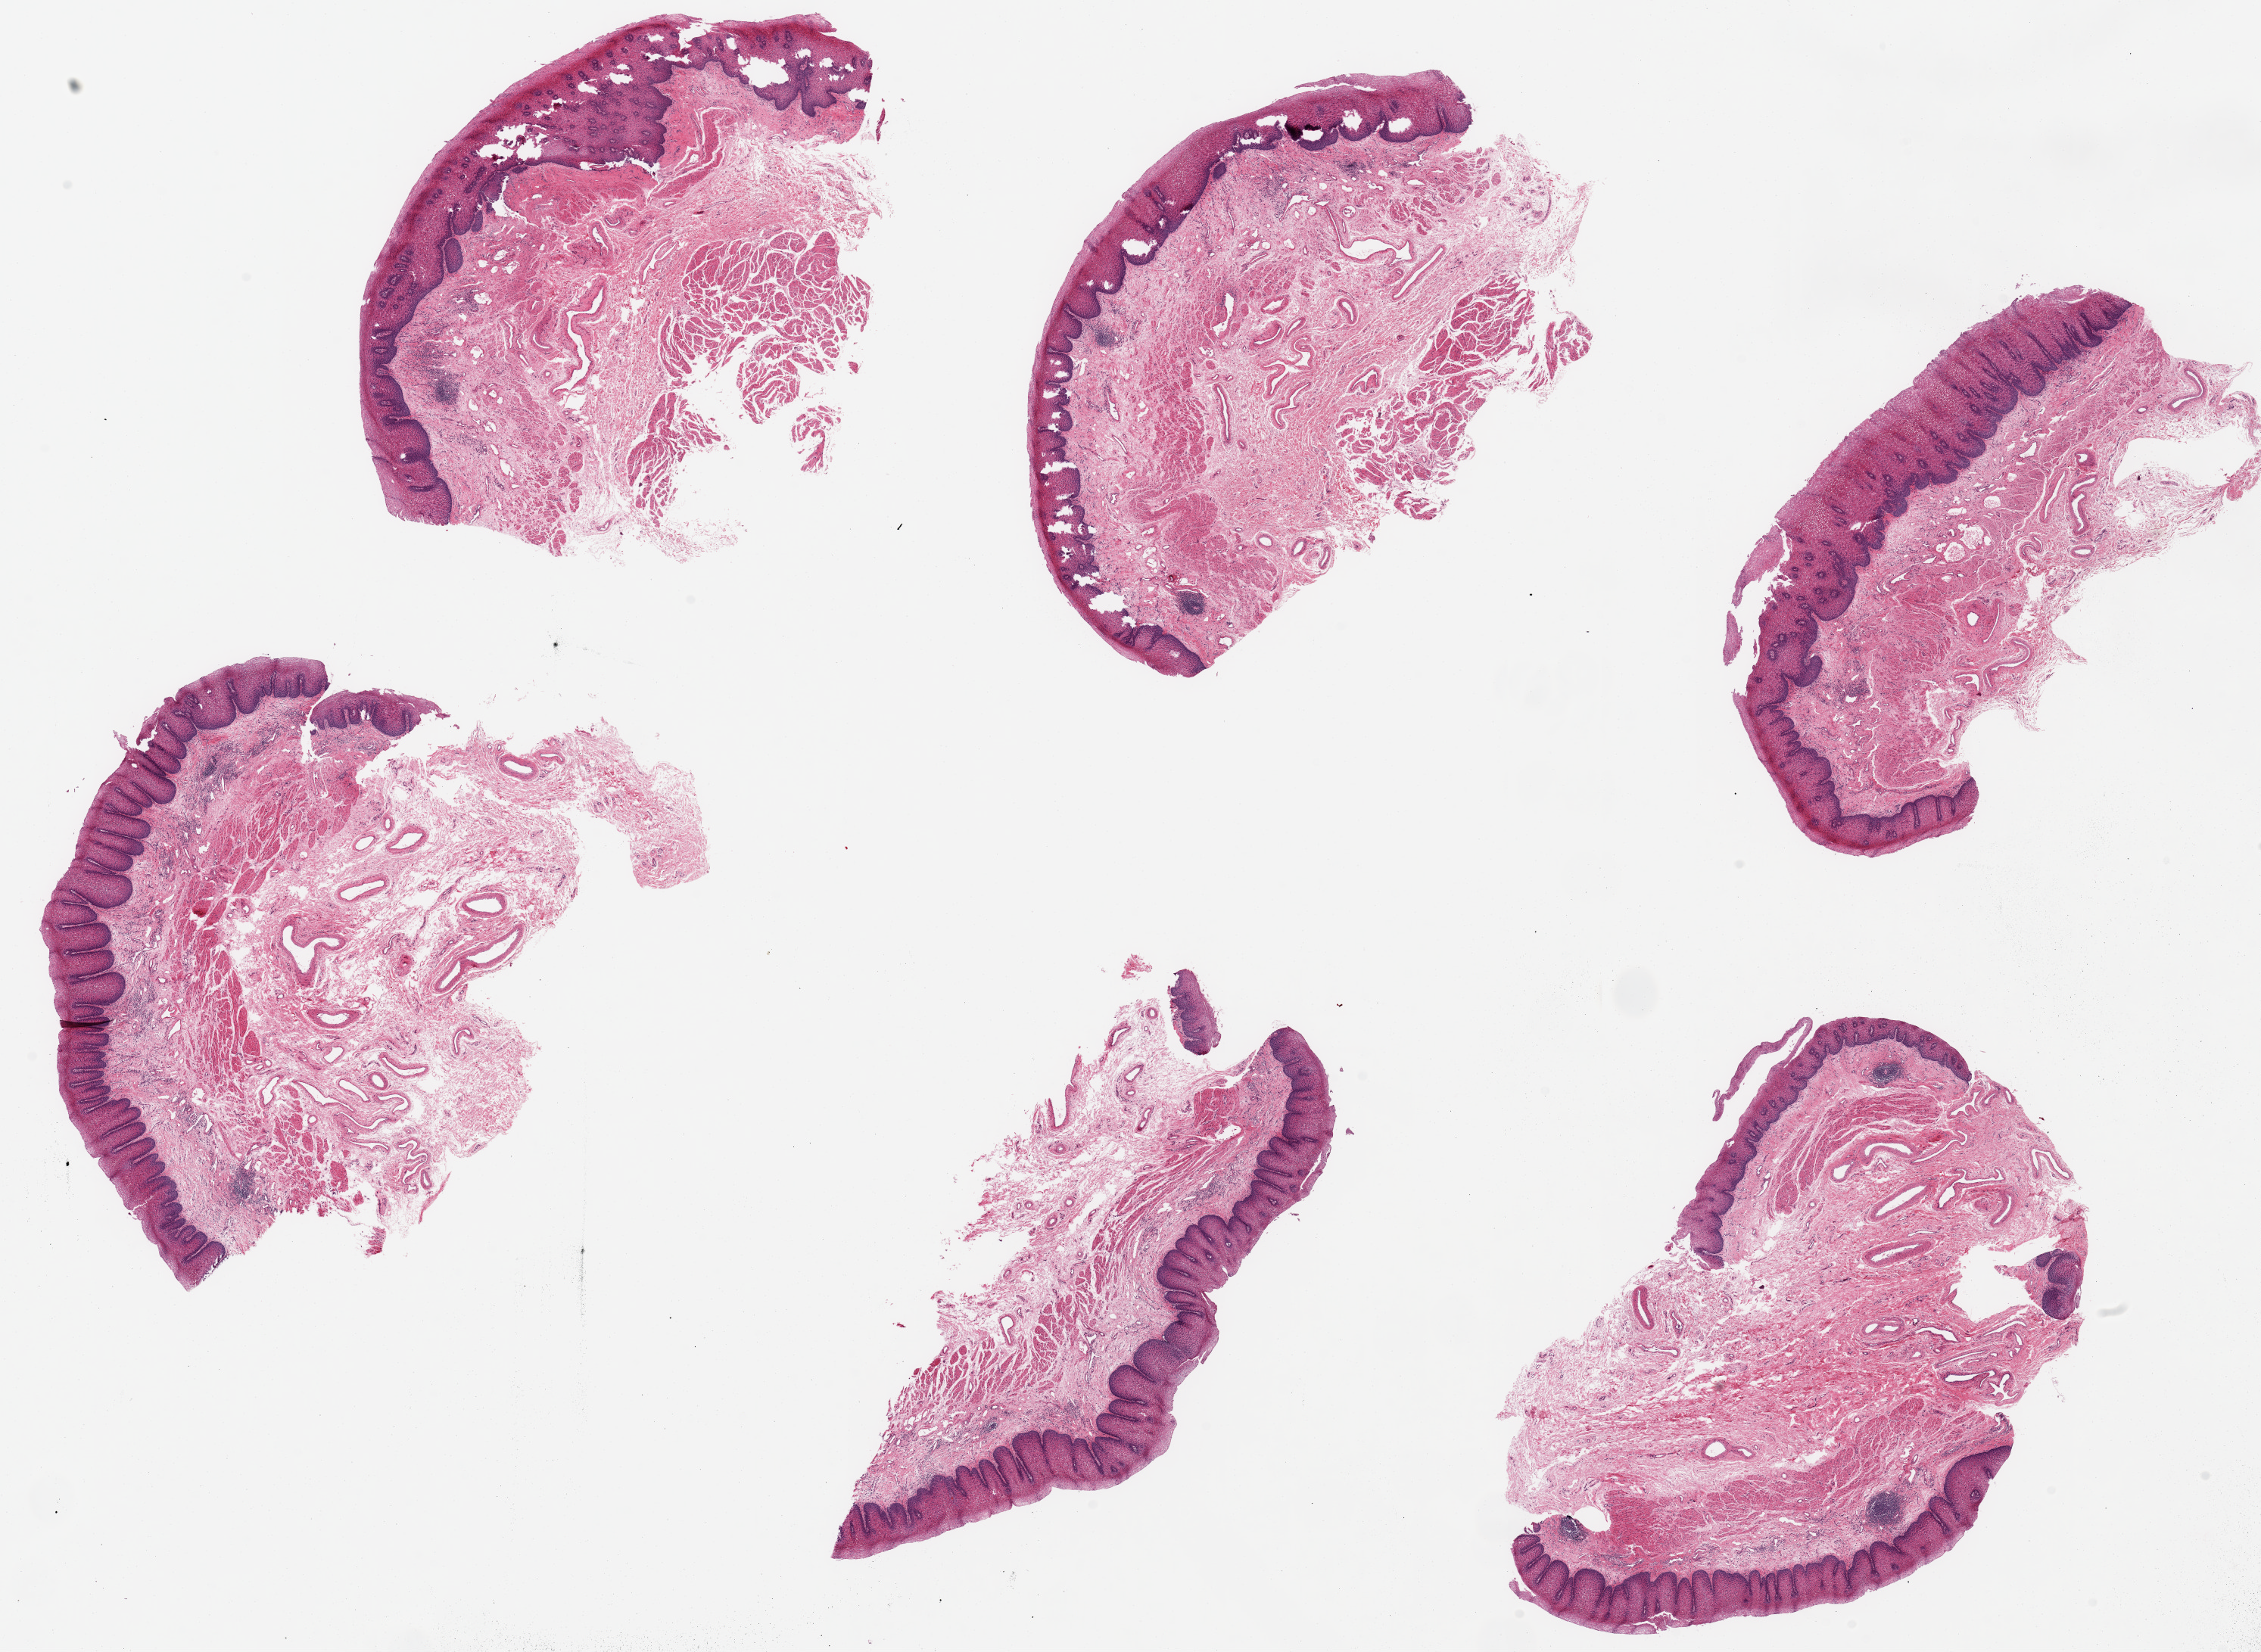
Haematoxylin and eosin whole-slide image — whole scanned area (about 23.6 x 17.3 mm) shown as a low-resolution overview; PAXgene-fixed paraffin-embedded (PFPE) section; section of esophageal mucous membrane (target tissue); tissue donor sample. Donor sex: male.
Review note (as recorded): 6 pieces up to 7x4 mm; all with slightly hyperplastic epithelium.